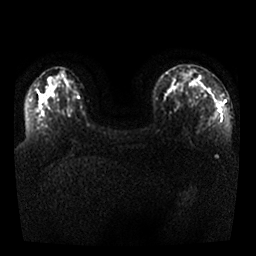
Breast MRI, one axial slice; position 11 of 25 along the scan axis; diffusion-weighted series; image 2 of 4 stored at this slice position (different b-values; order by instance number); 1.5 T; 4 mm slice thickness; 256 × 256 image matrix. Female patient.
Annotated regions visible in this slice (manually delineated by an expert):
- tumour on diffusion-weighted imaging: bounding box <177,70,204,87> (left, top, right, bottom; pixels)